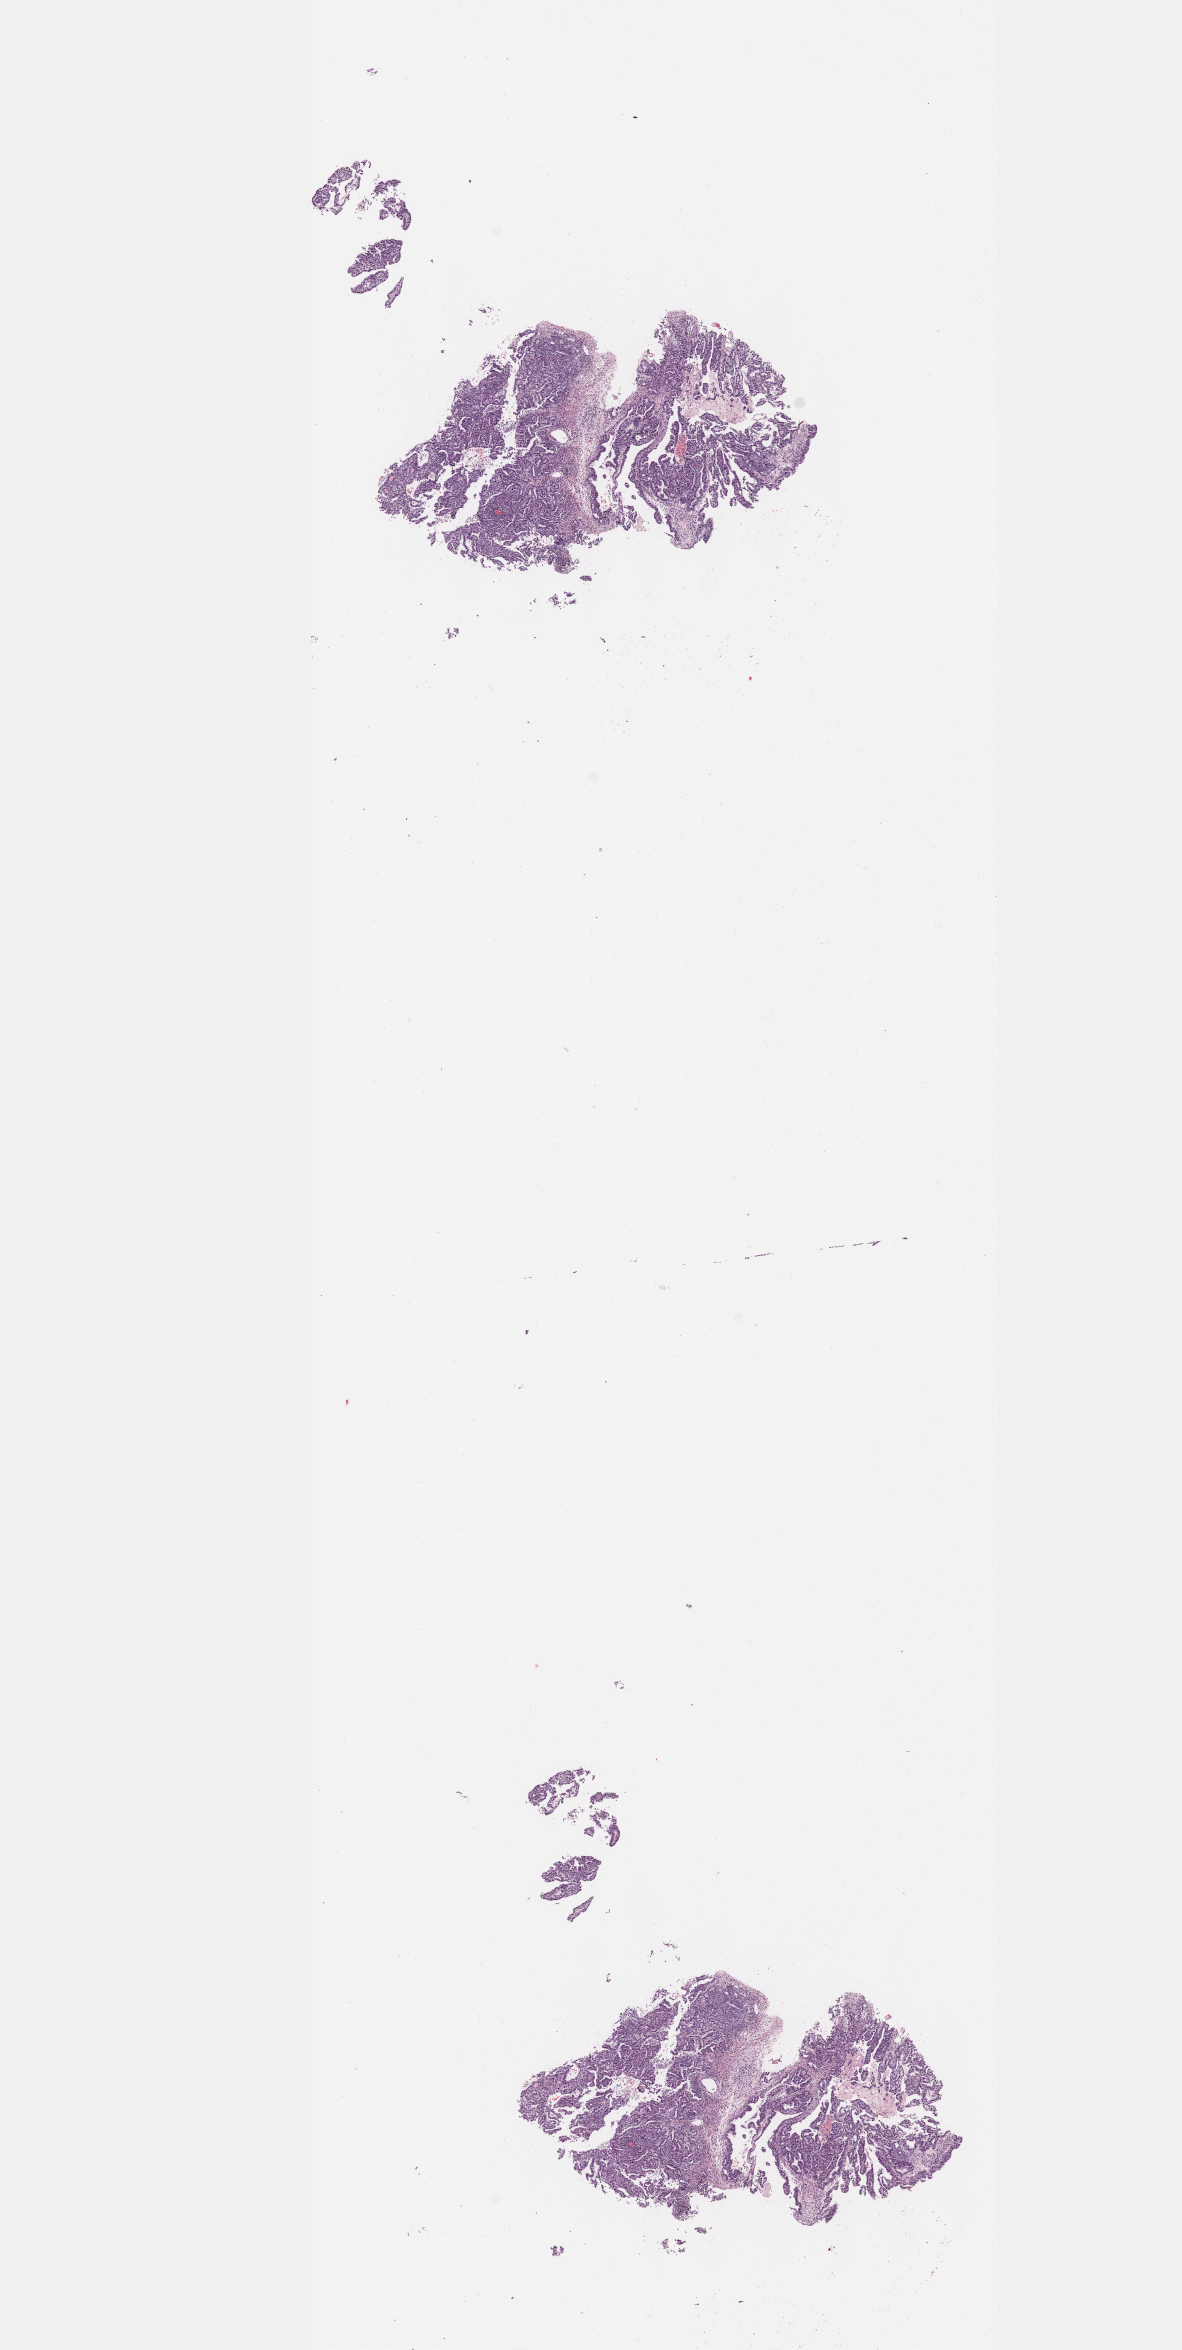
Whole-slide histology image, Hematoxylin and eosin (H&E) stained — shown as a low-resolution overview of the whole scanned area (about 9.6 x 19.0 mm, acquisition: 40x scan), frozen section, testis, primary tumour sample. Patient: male, age at initial diagnosis 67 years. Composition of this section per pathologist review: tumour cells 70%, tumour nuclei 70%, normal cells 0%, stromal cells 30%, necrosis 0%. Inflammatory infiltration, as recorded: lymphocyte infiltration 60%, monocyte infiltration 20%, neutrophil infiltration 10%.
AJCC pathologic stage: I (7th edition). Laterality: left. TNM: T2 NX M0. Diagnosis: Embryonal carcinoma, NOS.